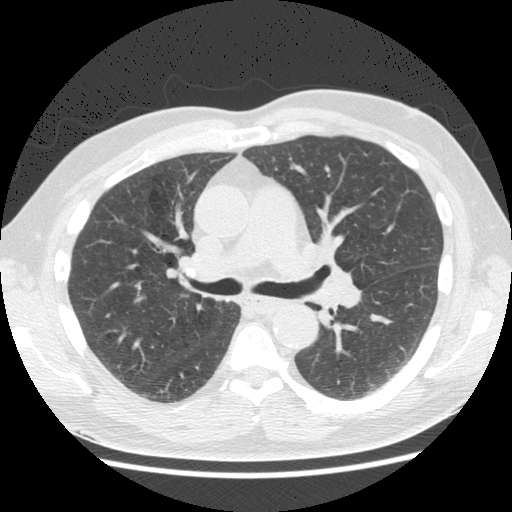
Low-dose screening chest CT, one axial slice; slice 100 of 161 in the series (ordered by position); lung window (W 1500 / L -600 HU); 512 × 512 image matrix, field of view 360 × 360 mm.
Annotated regions visible in this slice (manually delineated by an expert):
- lesion 1 (tumor, upper lobe of right lung): box from (x=132, y=293) to (x=146, y=305) px